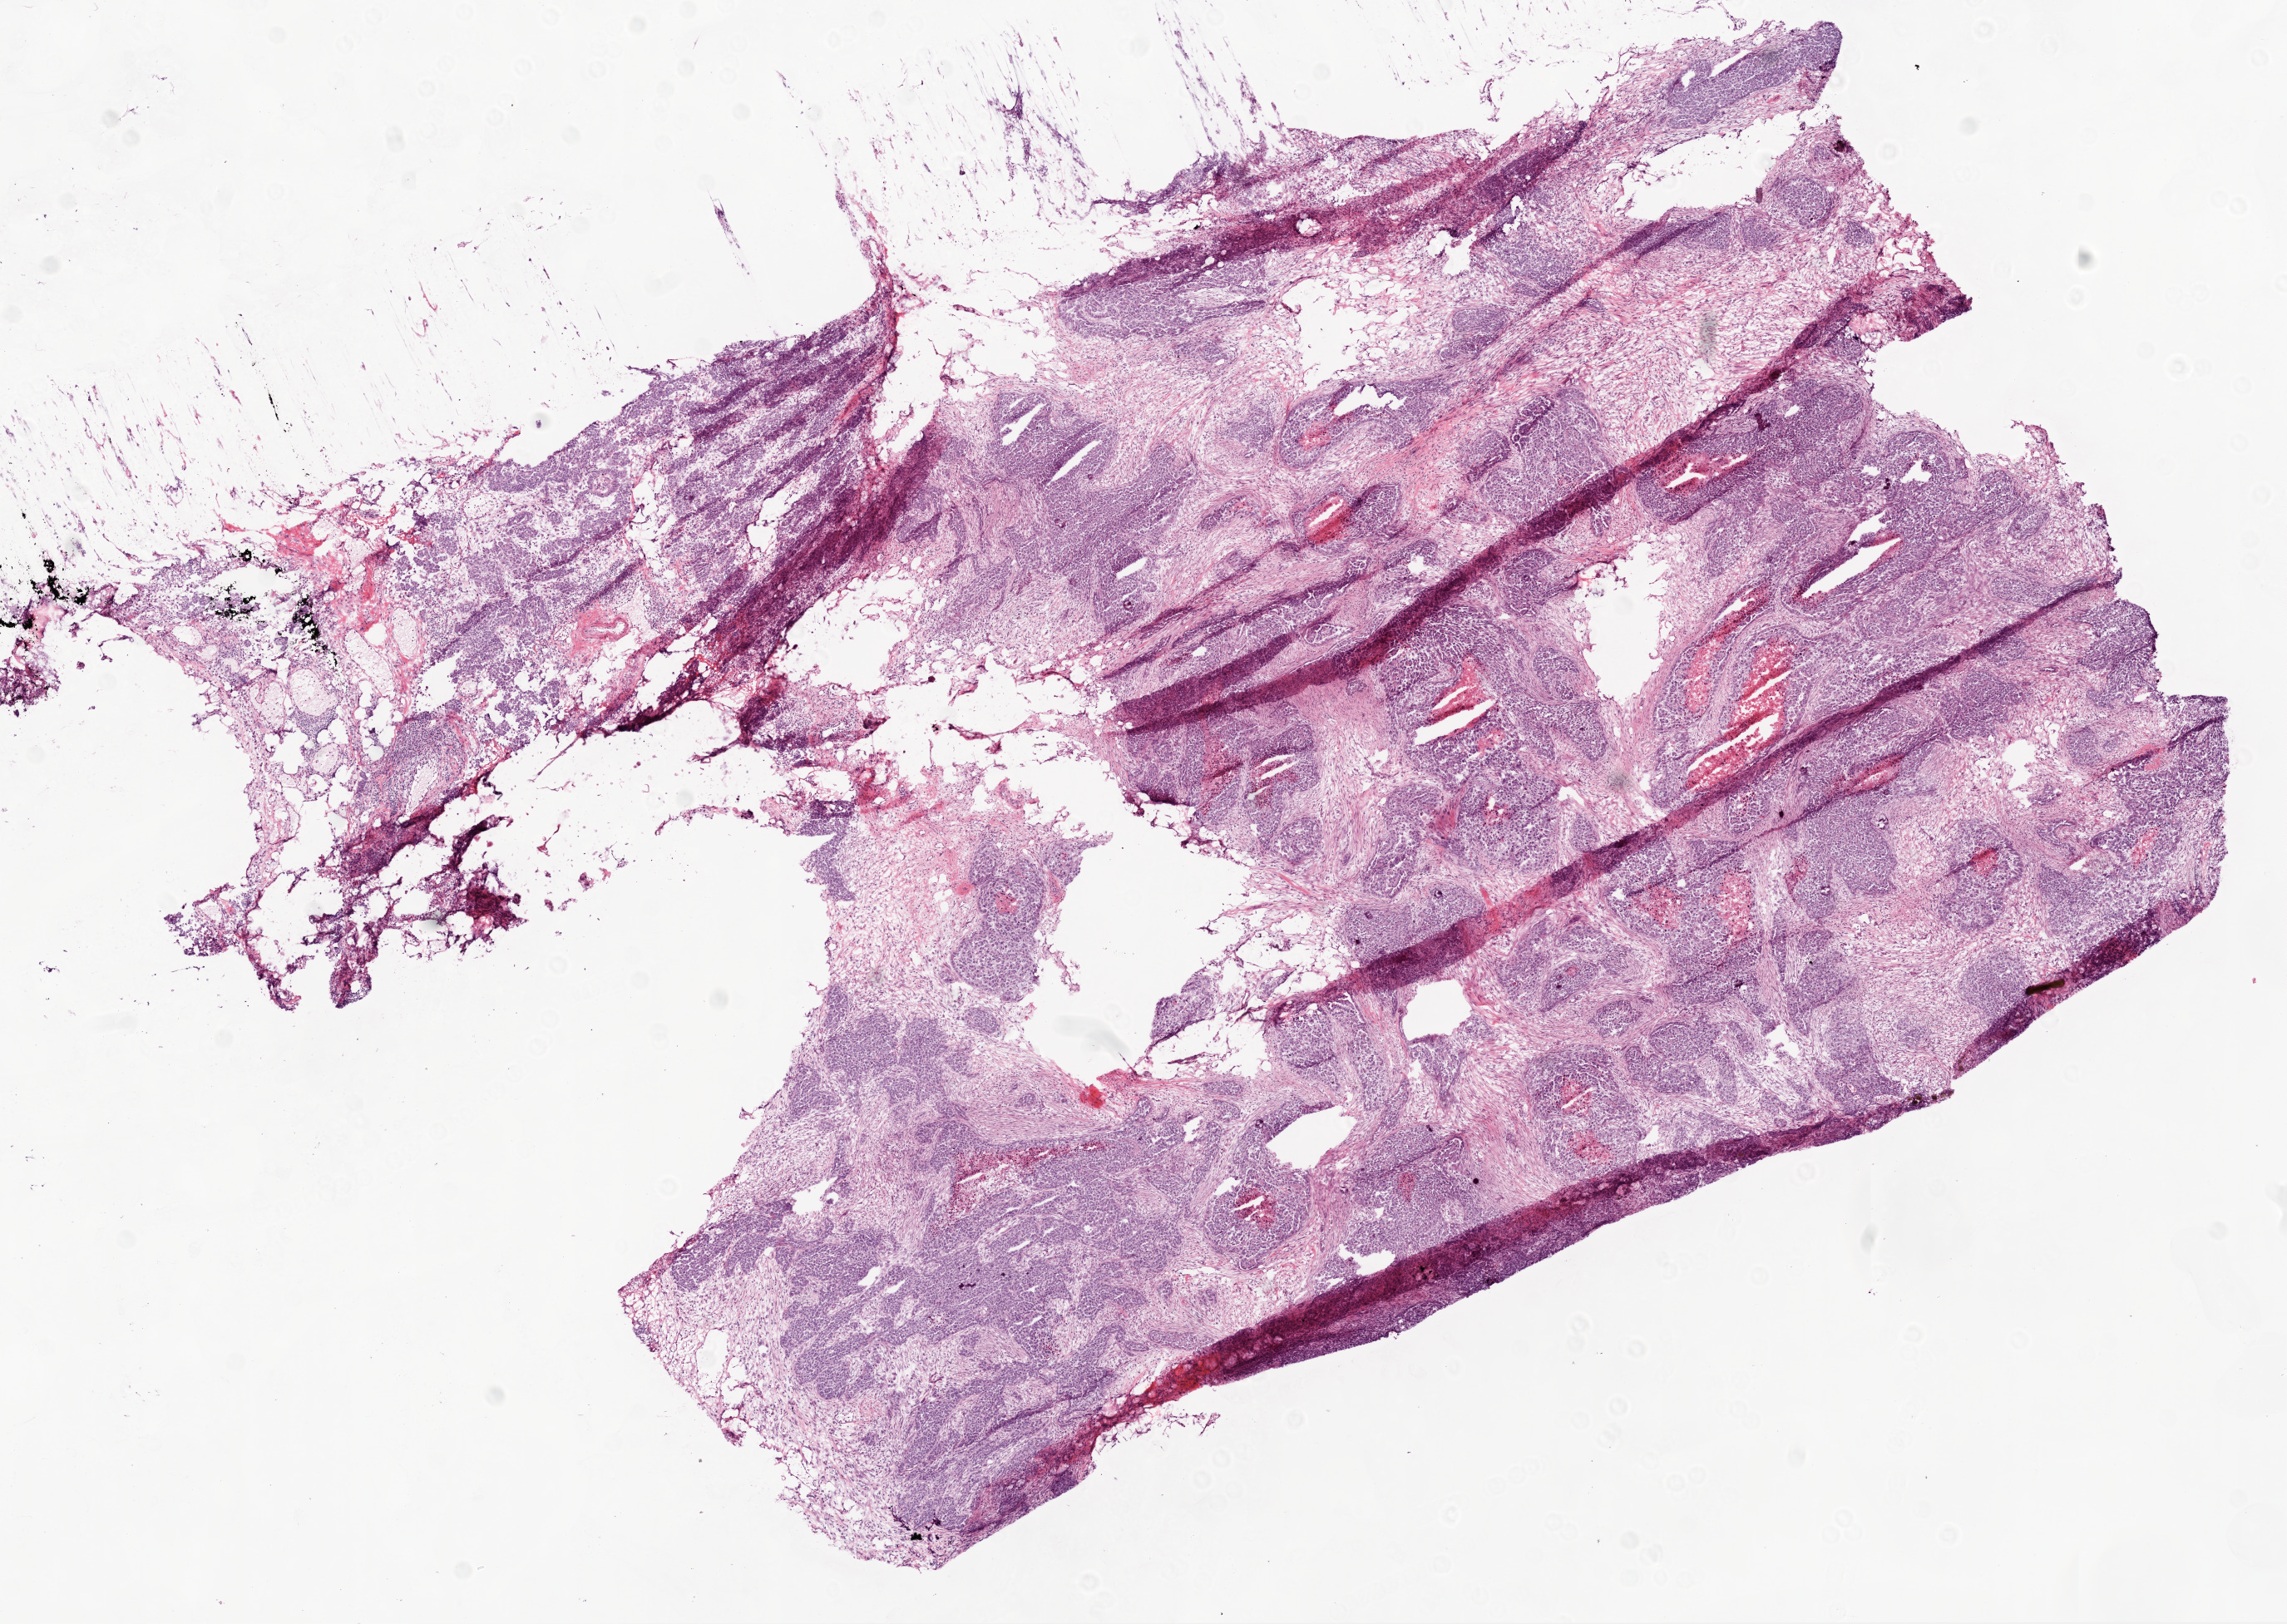
H&E-stained whole-slide image — a low-resolution overview of the entire scanned area, about 11.0 x 7.8 mm (acquisition: 20x scan), frozen section from the bottom of the tissue portion, primary tumour sample from the ovary. Female patient; age at initial diagnosis 57 years. Slide review estimates, as recorded: tumour cells 80%, tumour nuclei 85%.
Diagnosis: Serous cystadenocarcinoma, NOS.